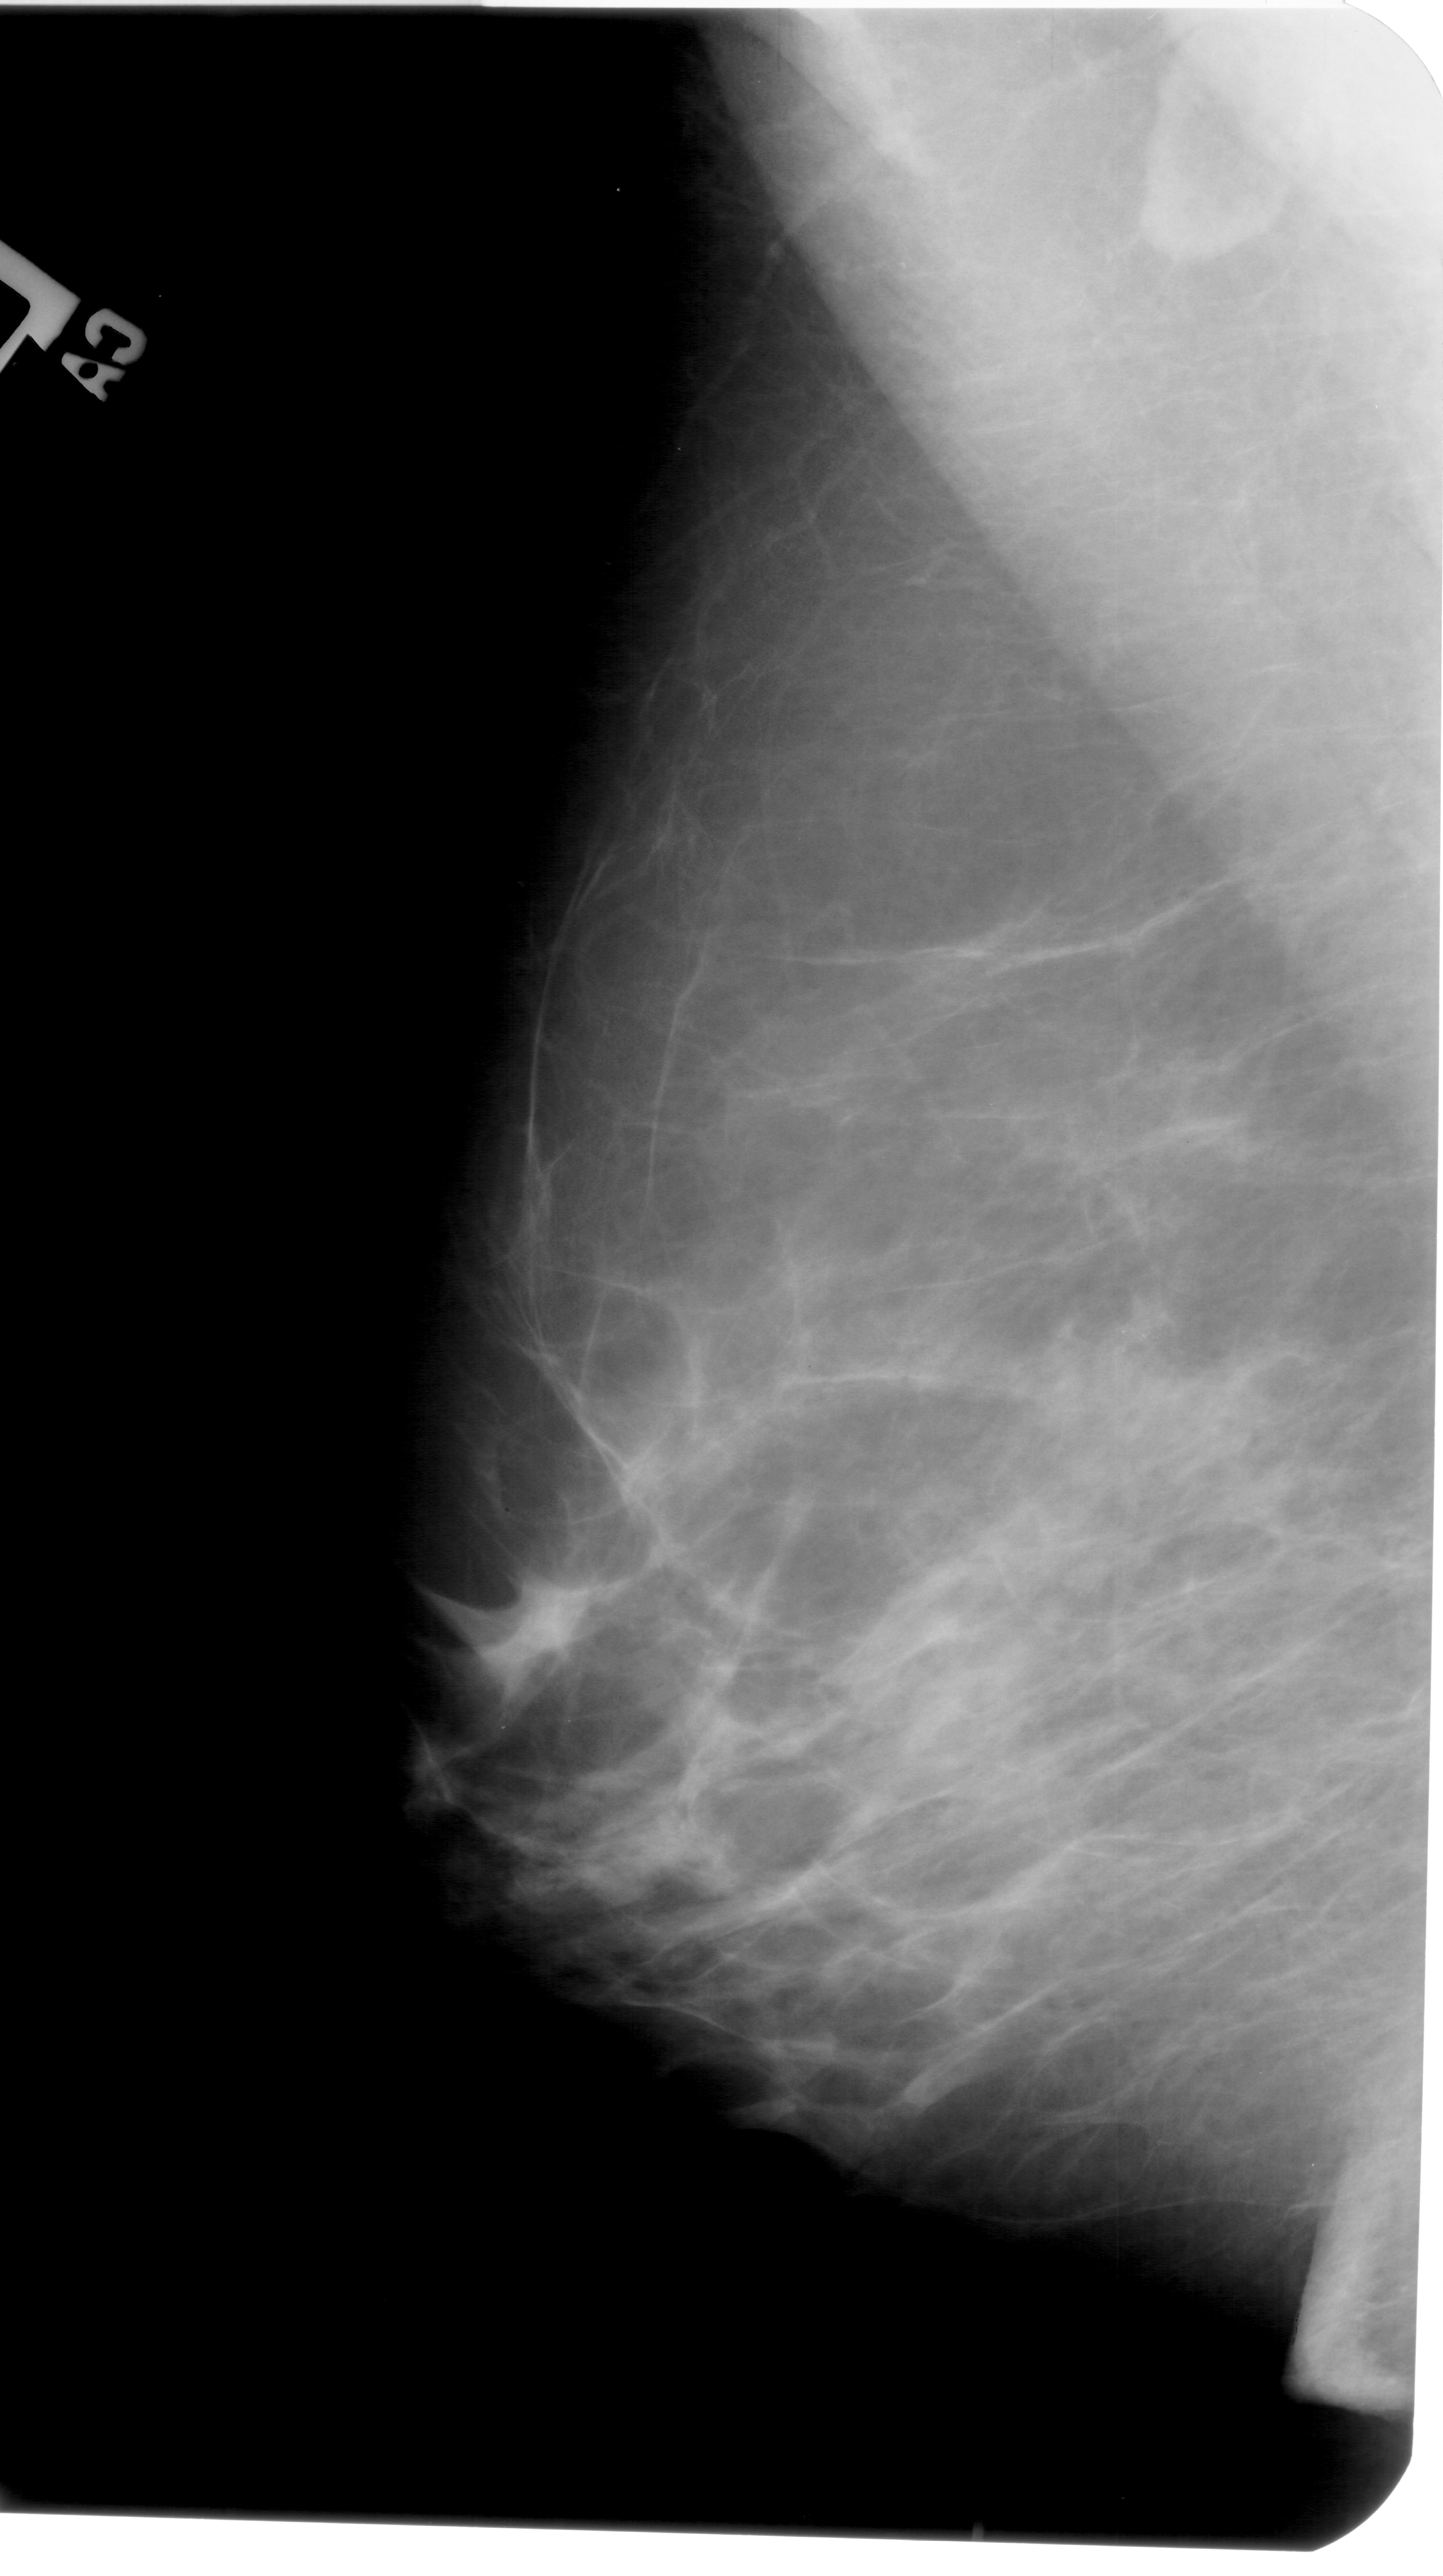
Digitized screen-film mammogram. Left breast. MLO view. Breast composition: heterogeneously dense (BI-RADS density category 3 of 4). 1443 × 2576 image matrix.
Expert-marked regions of interest on this film, with their recorded descriptors:
- calcifications, morphology pleomorphic, distribution clustered; BI-RADS assessment category 4; pathology result (as recorded, not read from the image): benign: bounding box <1029,1262,1210,1418> (left, top, right, bottom; pixels)